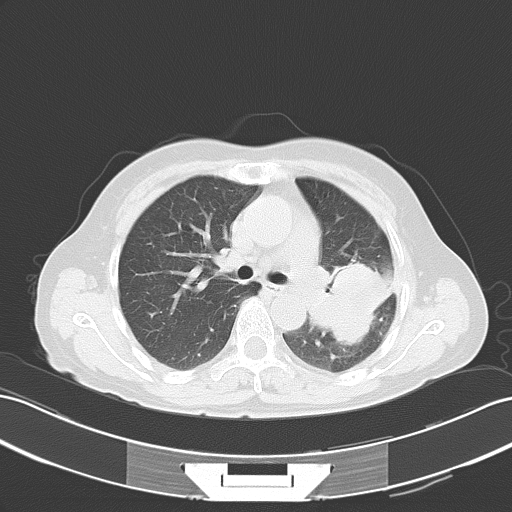
Chest CT, one axial slice; slice 32 of 51 in the series (ordered by position); reconstruction kernel B70f; lung window (W 1500 / L -600 HU); 5 mm slice thickness; 512 × 512 image matrix. Patient: female, 54 years. From the clinical record (not read from this slice): clinical TNM (as recorded): T3 N1 M0.
Annotated regions visible in this slice (rectangle marked by the reading radiologist):
- lung tumour (recorded histology: adenocarcinoma): box from (x=327, y=253) to (x=398, y=345) px